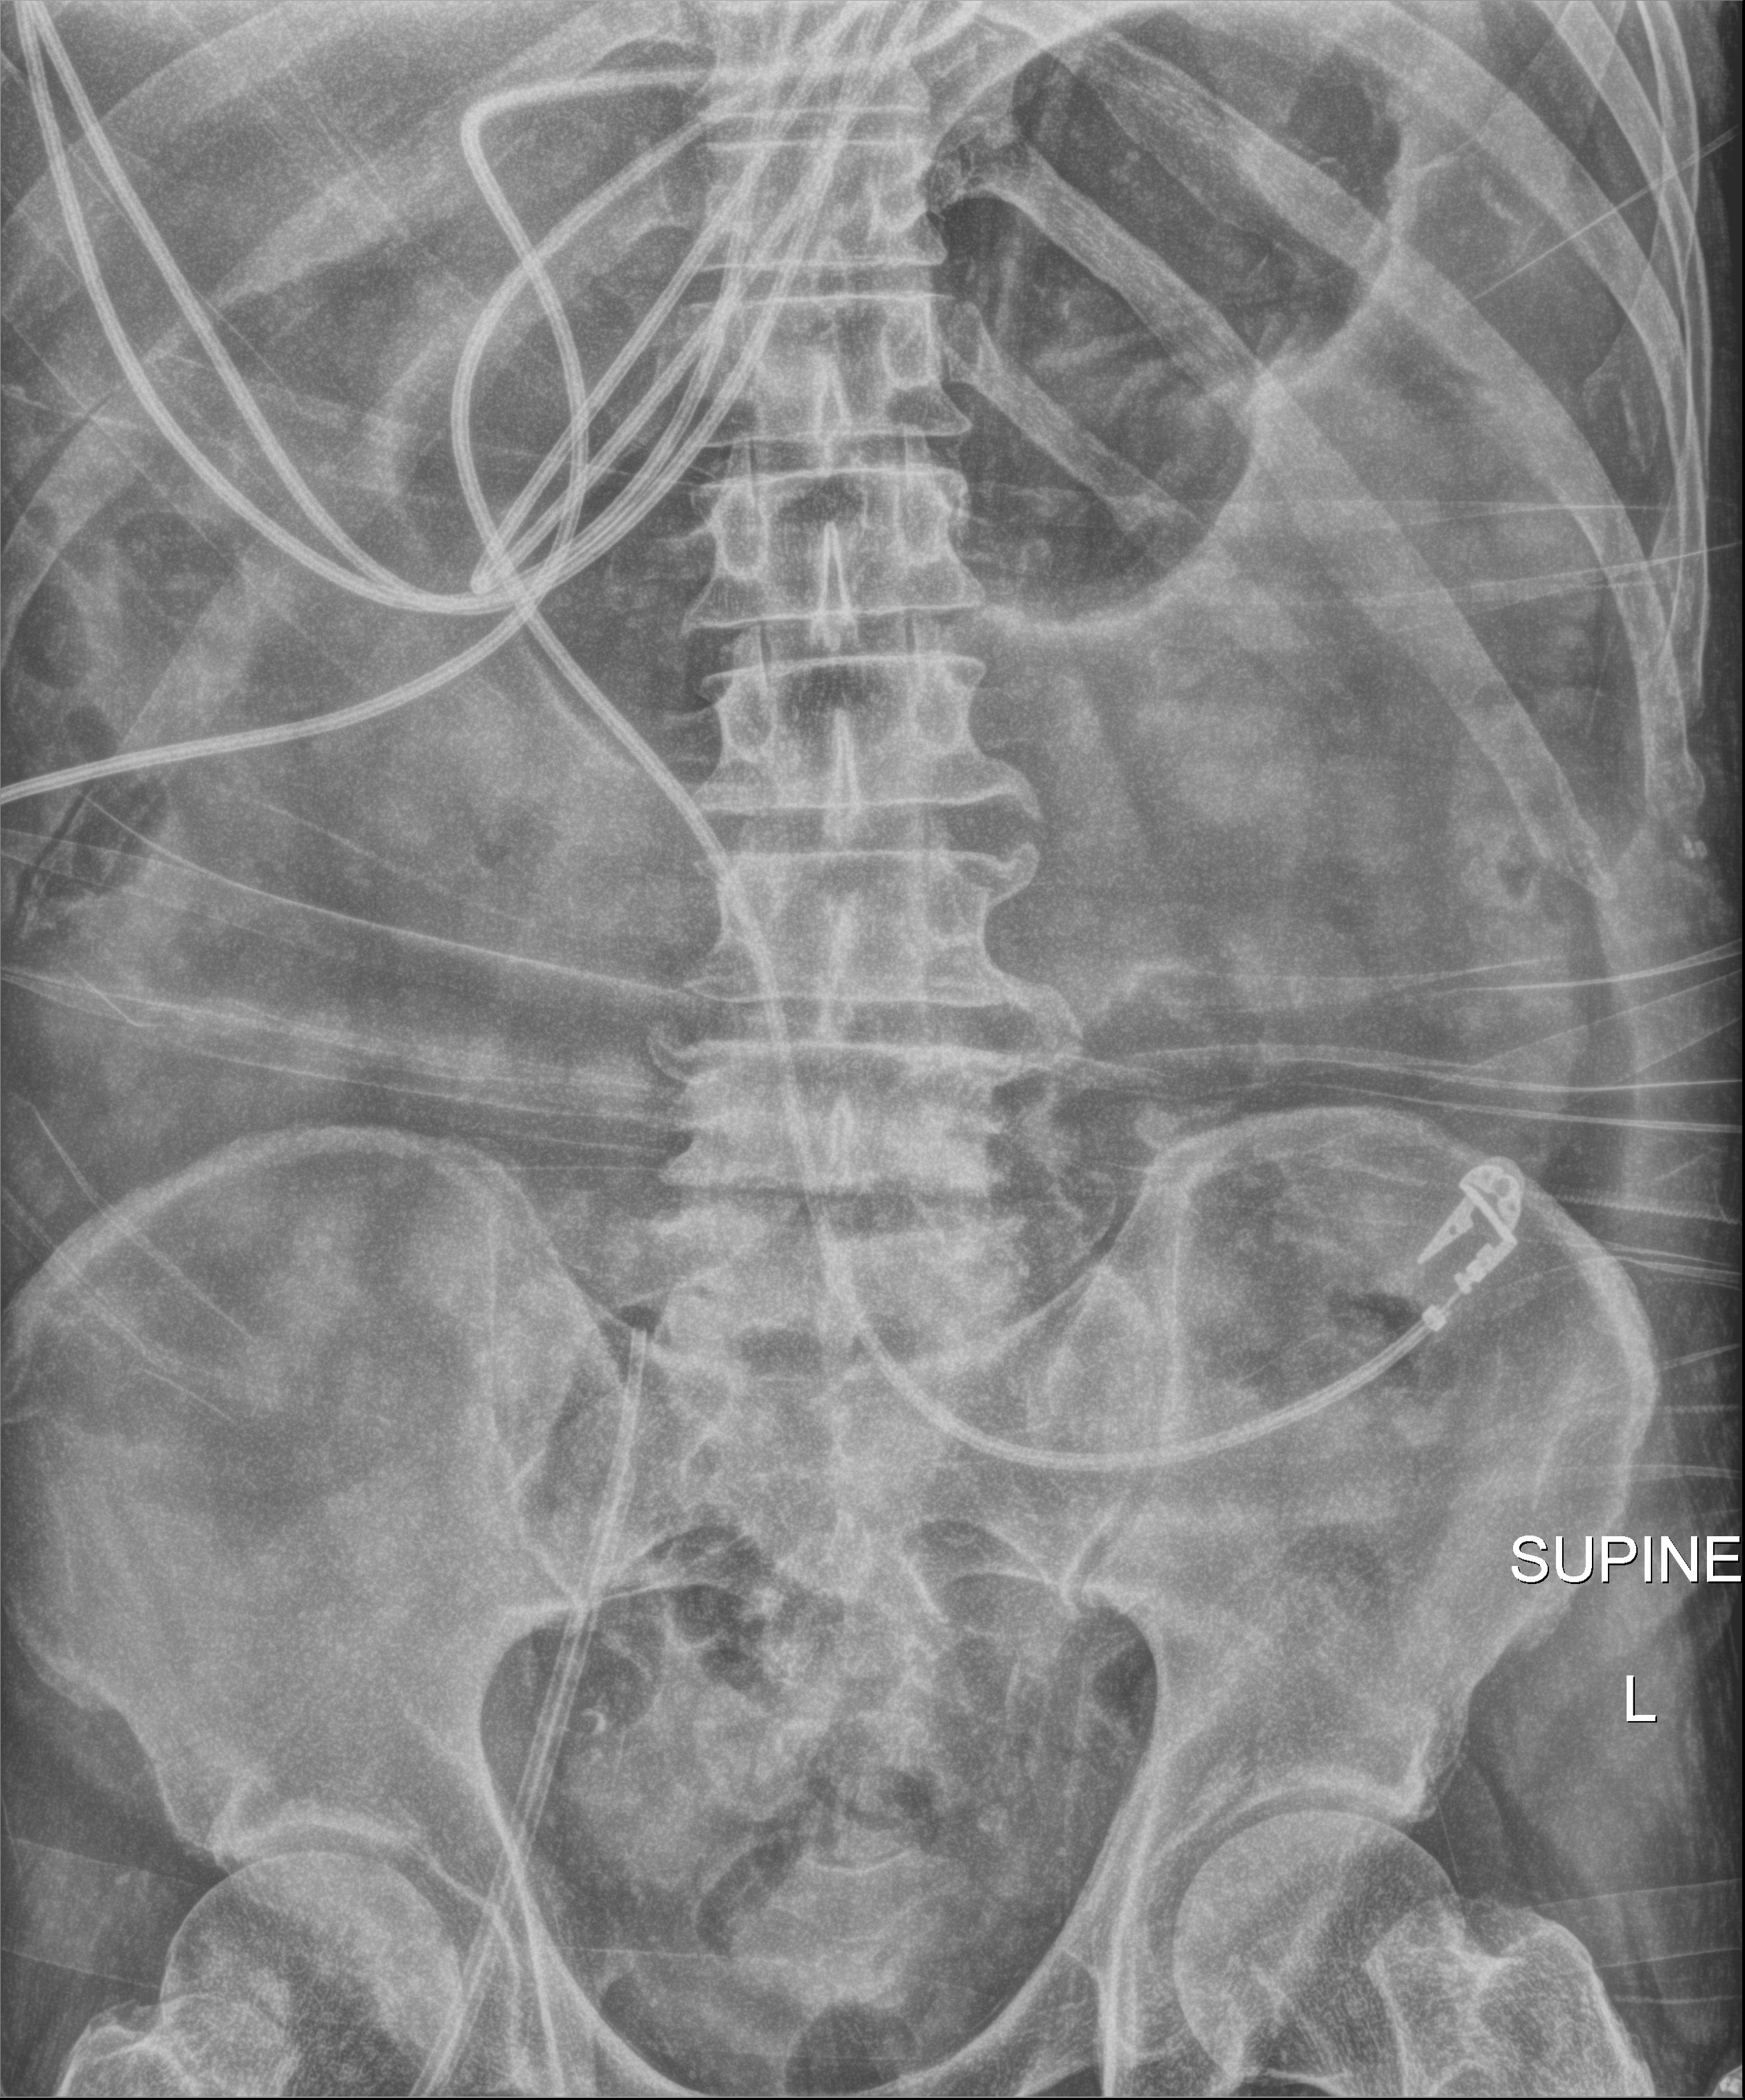
Portable abdomen radiograph; anteroposterior (AP) projection. Patient hospitalised with COVID-19; male, aged 60–74 years.
Hospital-stay facts (about this admission, not read from this image; timing relative to this image not recorded):
- admitted to intensive care during this hospital stay: yes